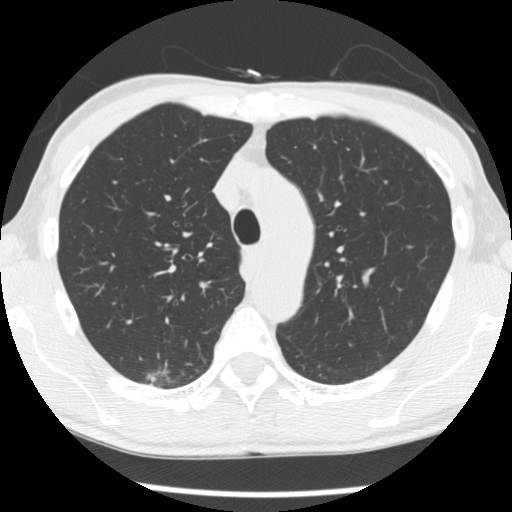
Low-dose screening chest CT, axial slice, baseline annual screen, lung window (W 1500 / L -600 HU), slice 75 of 277 in the series. Male participant, aged 66 years at enrolment.
- Expert reader's lesion annotation, box from (x=135, y=356) to (x=186, y=394) px.
- The screening reader recorded 4 non-calcified nodules or masses ≥4 mm on this exam; which of them this box marks is not recorded.
- Official screen result: positive, change unspecified: nodule(s) >= 4 mm or enlarging nodule(s), mass(es), or other non-specific abnormalities suspicious for lung cancer.